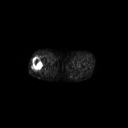
FDG PET of an extremity soft-tissue mass (from a PET/CT study), one axial slice; position 240 of 267 along the scan axis; 3.27 mm slice thickness; 128 × 128 image matrix, field of view 700 × 700 mm. Male patient, age 43 years. Case-level facts recorded for this patient, not image findings: histological type: poorly differentiated synovial sarcoma; grade: high; site of the primary tumour: right buttock.
Structures marked on this image (expert contour drawn on MRI and transferred to this co-registered scan by the dataset authors):
- gross tumour volume including surrounding oedema: bounding box (x1, y1, x2, y2) in pixels: (31, 58, 43, 71)
- gross tumour volume (mass): (32, 58, 43, 71)